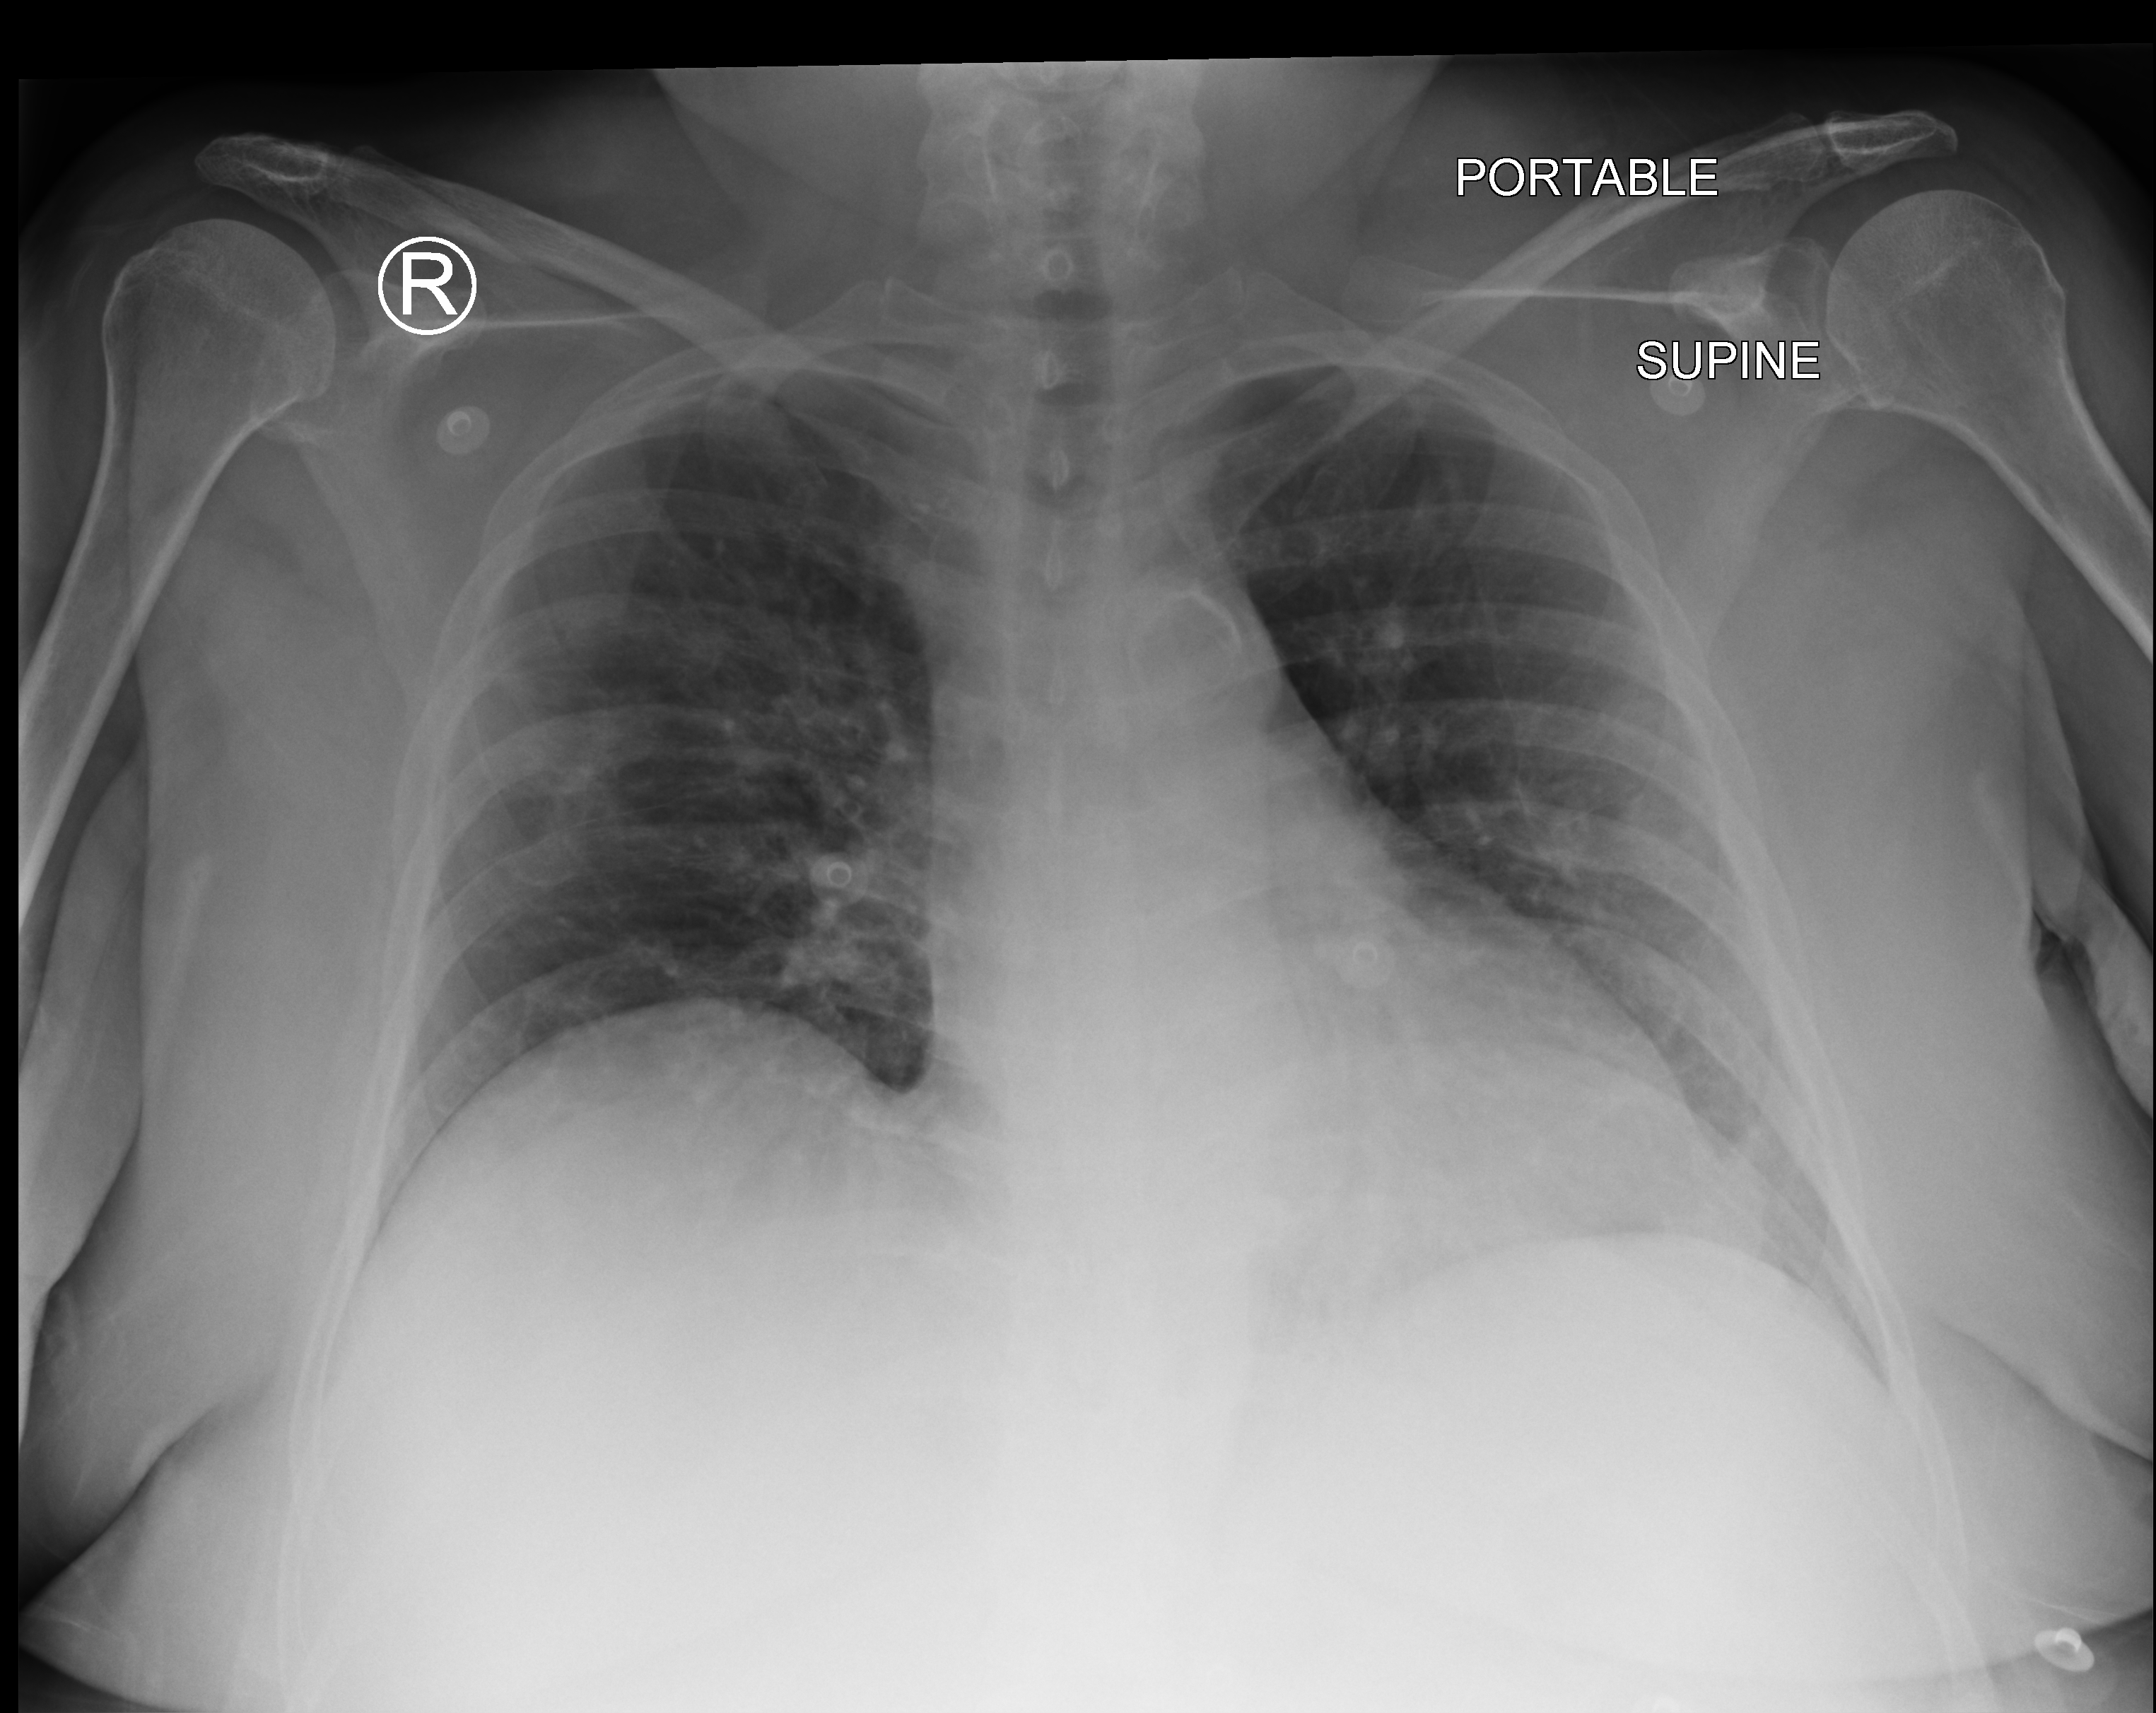
Portable chest radiograph, anteroposterior (AP) projection. Patient hospitalised with COVID-19; female, aged 60–74 years.
Admission-level facts for this patient (not findings on this image; timing relative to this image not recorded):
- admitted to intensive care during this hospital stay: no
- mechanically ventilated during this hospital stay: no